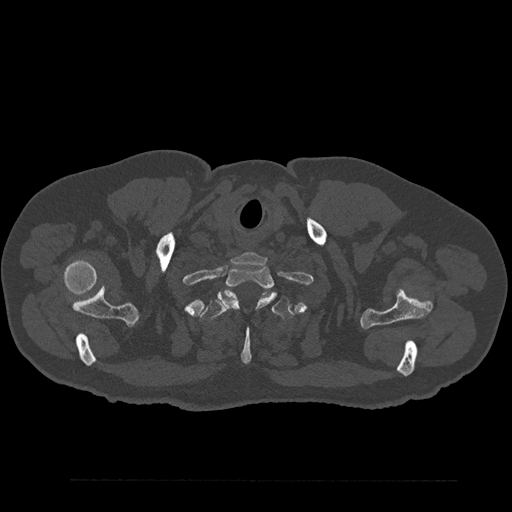
CT including the spine, one axial slice. Slice 741 of 797 in the series (ordered by position). Reconstruction kernel Br40s/3. 120 kVp. Bone window (W 1800 / L 400 HU). 512 × 512 image matrix, field of view 430 × 430 mm. Male patient, age 61 years. Case-level facts recorded for this patient, not image findings: primary cancer: prostate.
Outlined on this slice (semi-automatically segmented with operator editing):
- T1 vertebra: bounding box [x1, y1, x2, y2] px = [218, 266, 276, 309]
- T2 vertebra: [200, 291, 295, 365]